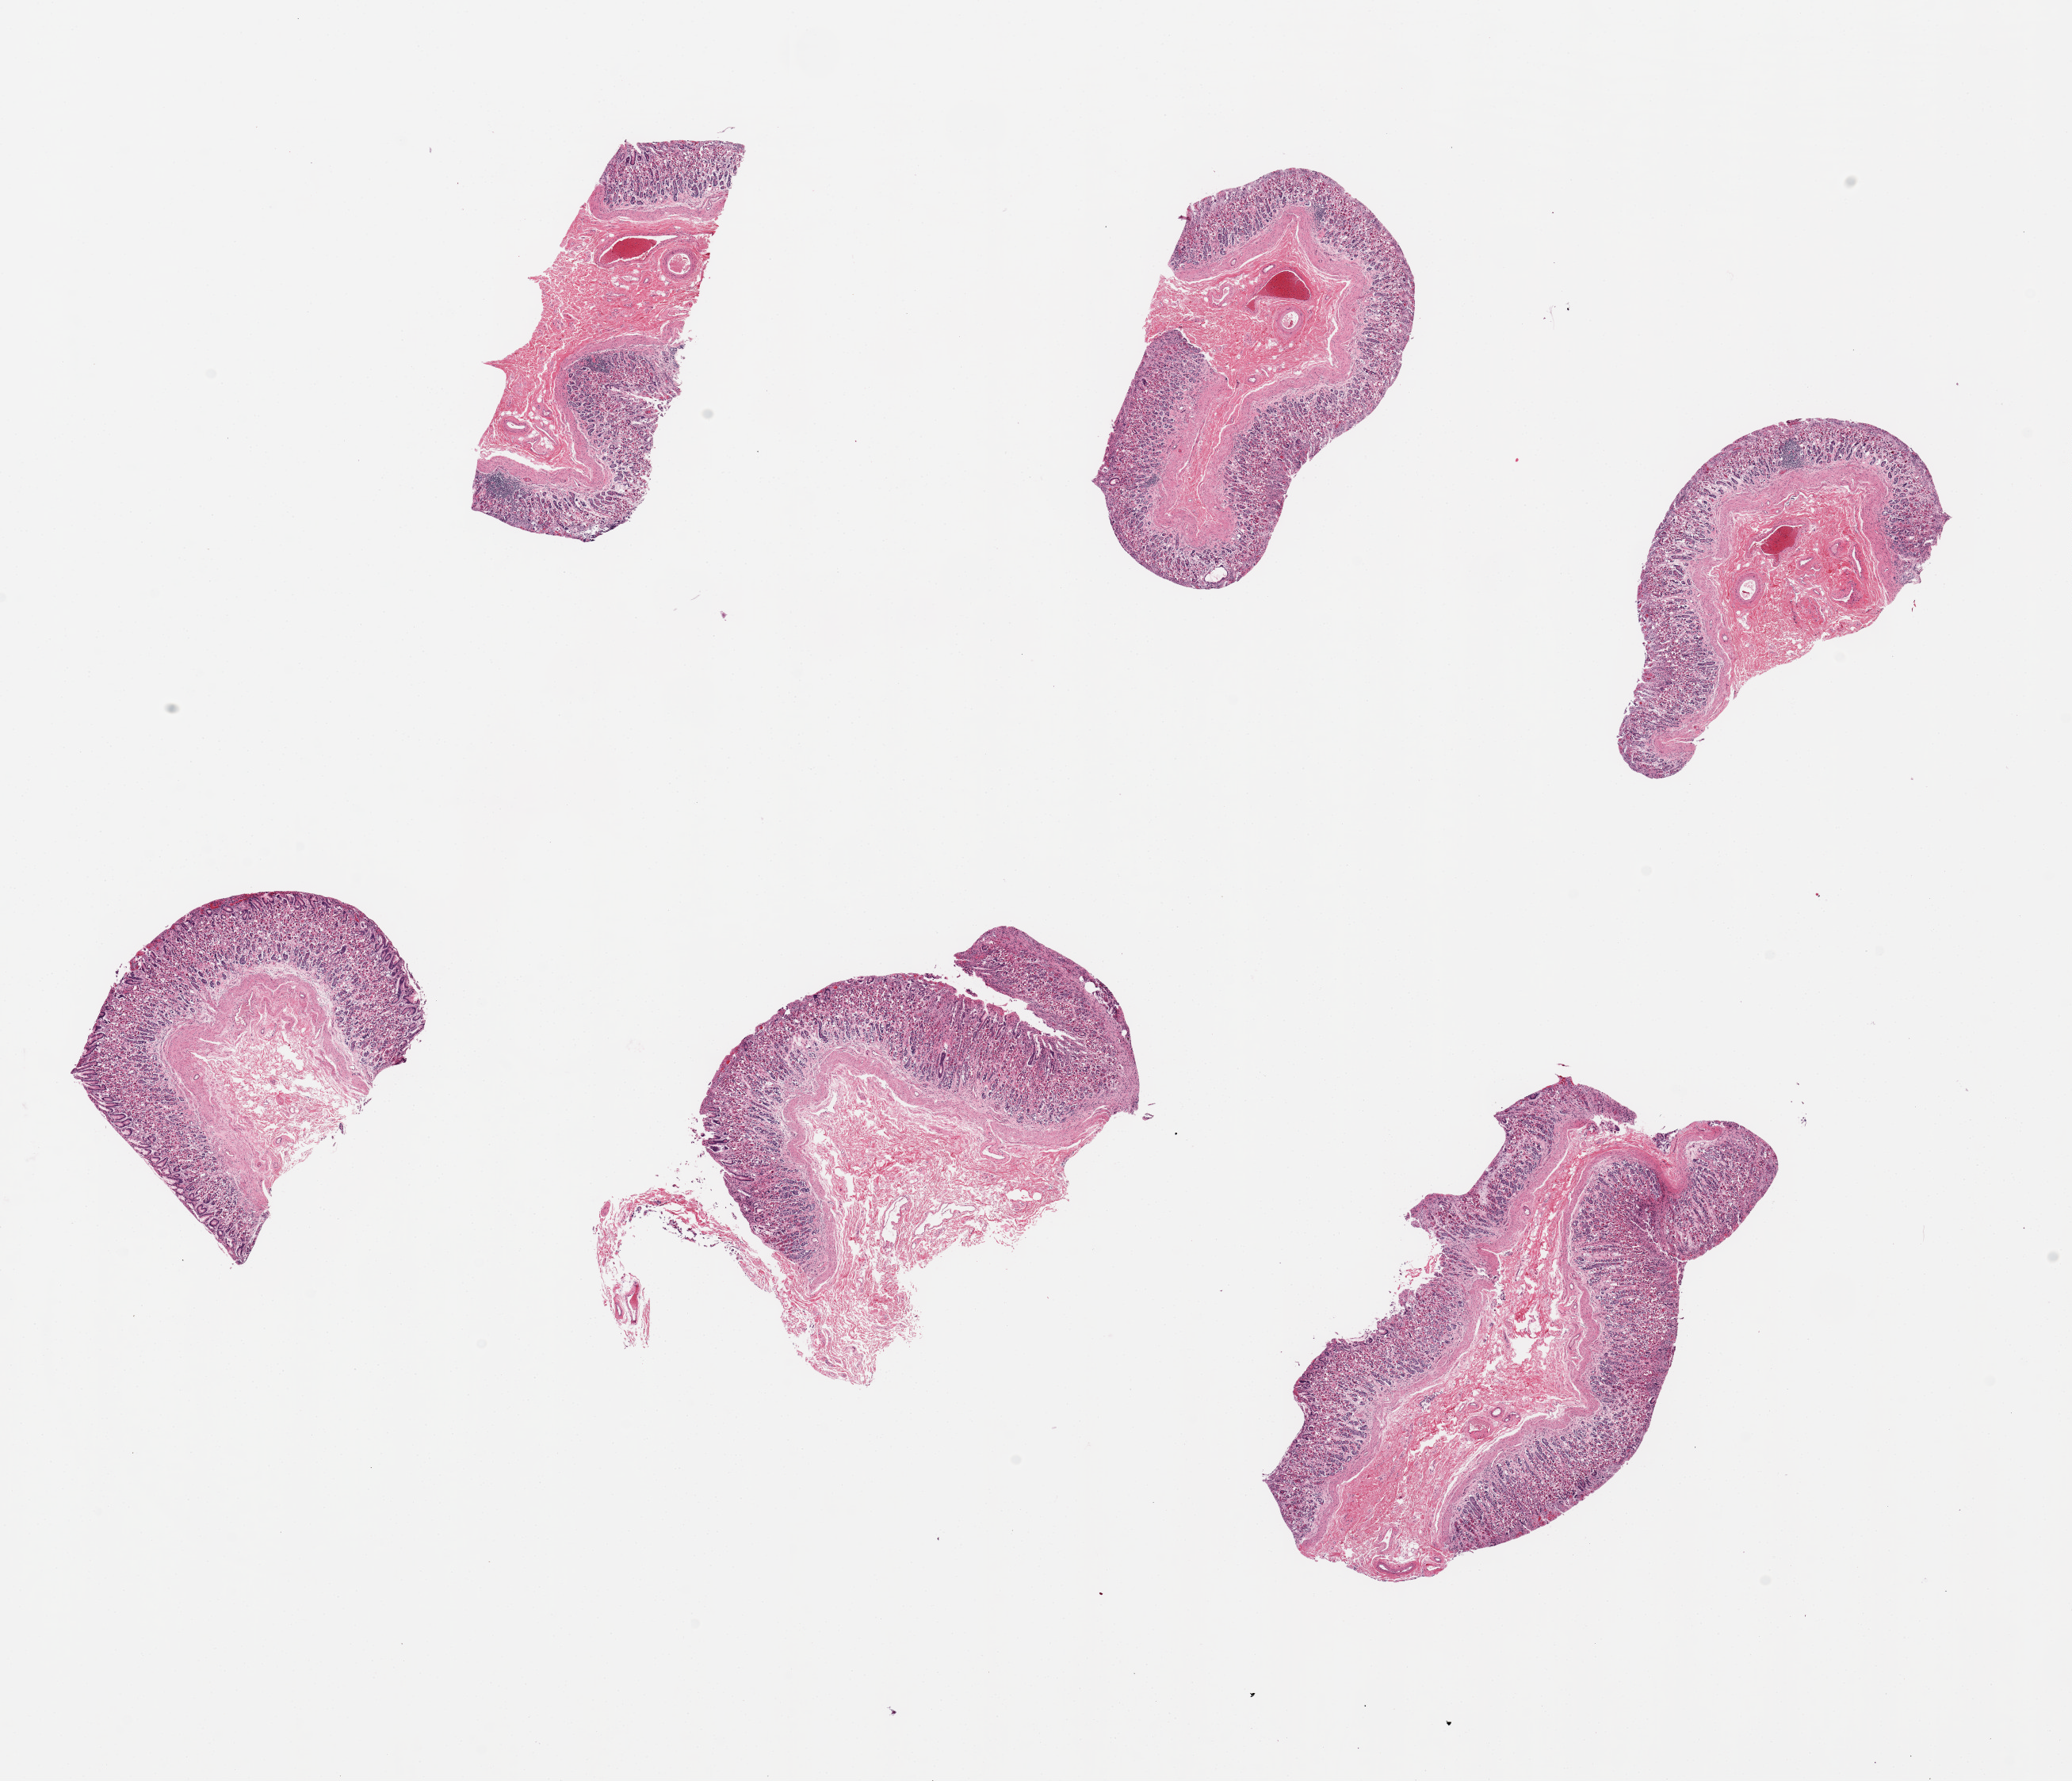
Digitized haematoxylin and eosin-stained section, brightfield — whole scanned area (about 20.7 x 17.8 mm, from a 20x scan) shown as a low-resolution overview; PAXgene-fixed, paraffin-embedded tissue; sampled site (target tissue): stomach; donor tissue sample. Donor sex: female.
Review note (as recorded): 6 pieces, up to 6x3mm; mucosa and submucosa, no muscularis.